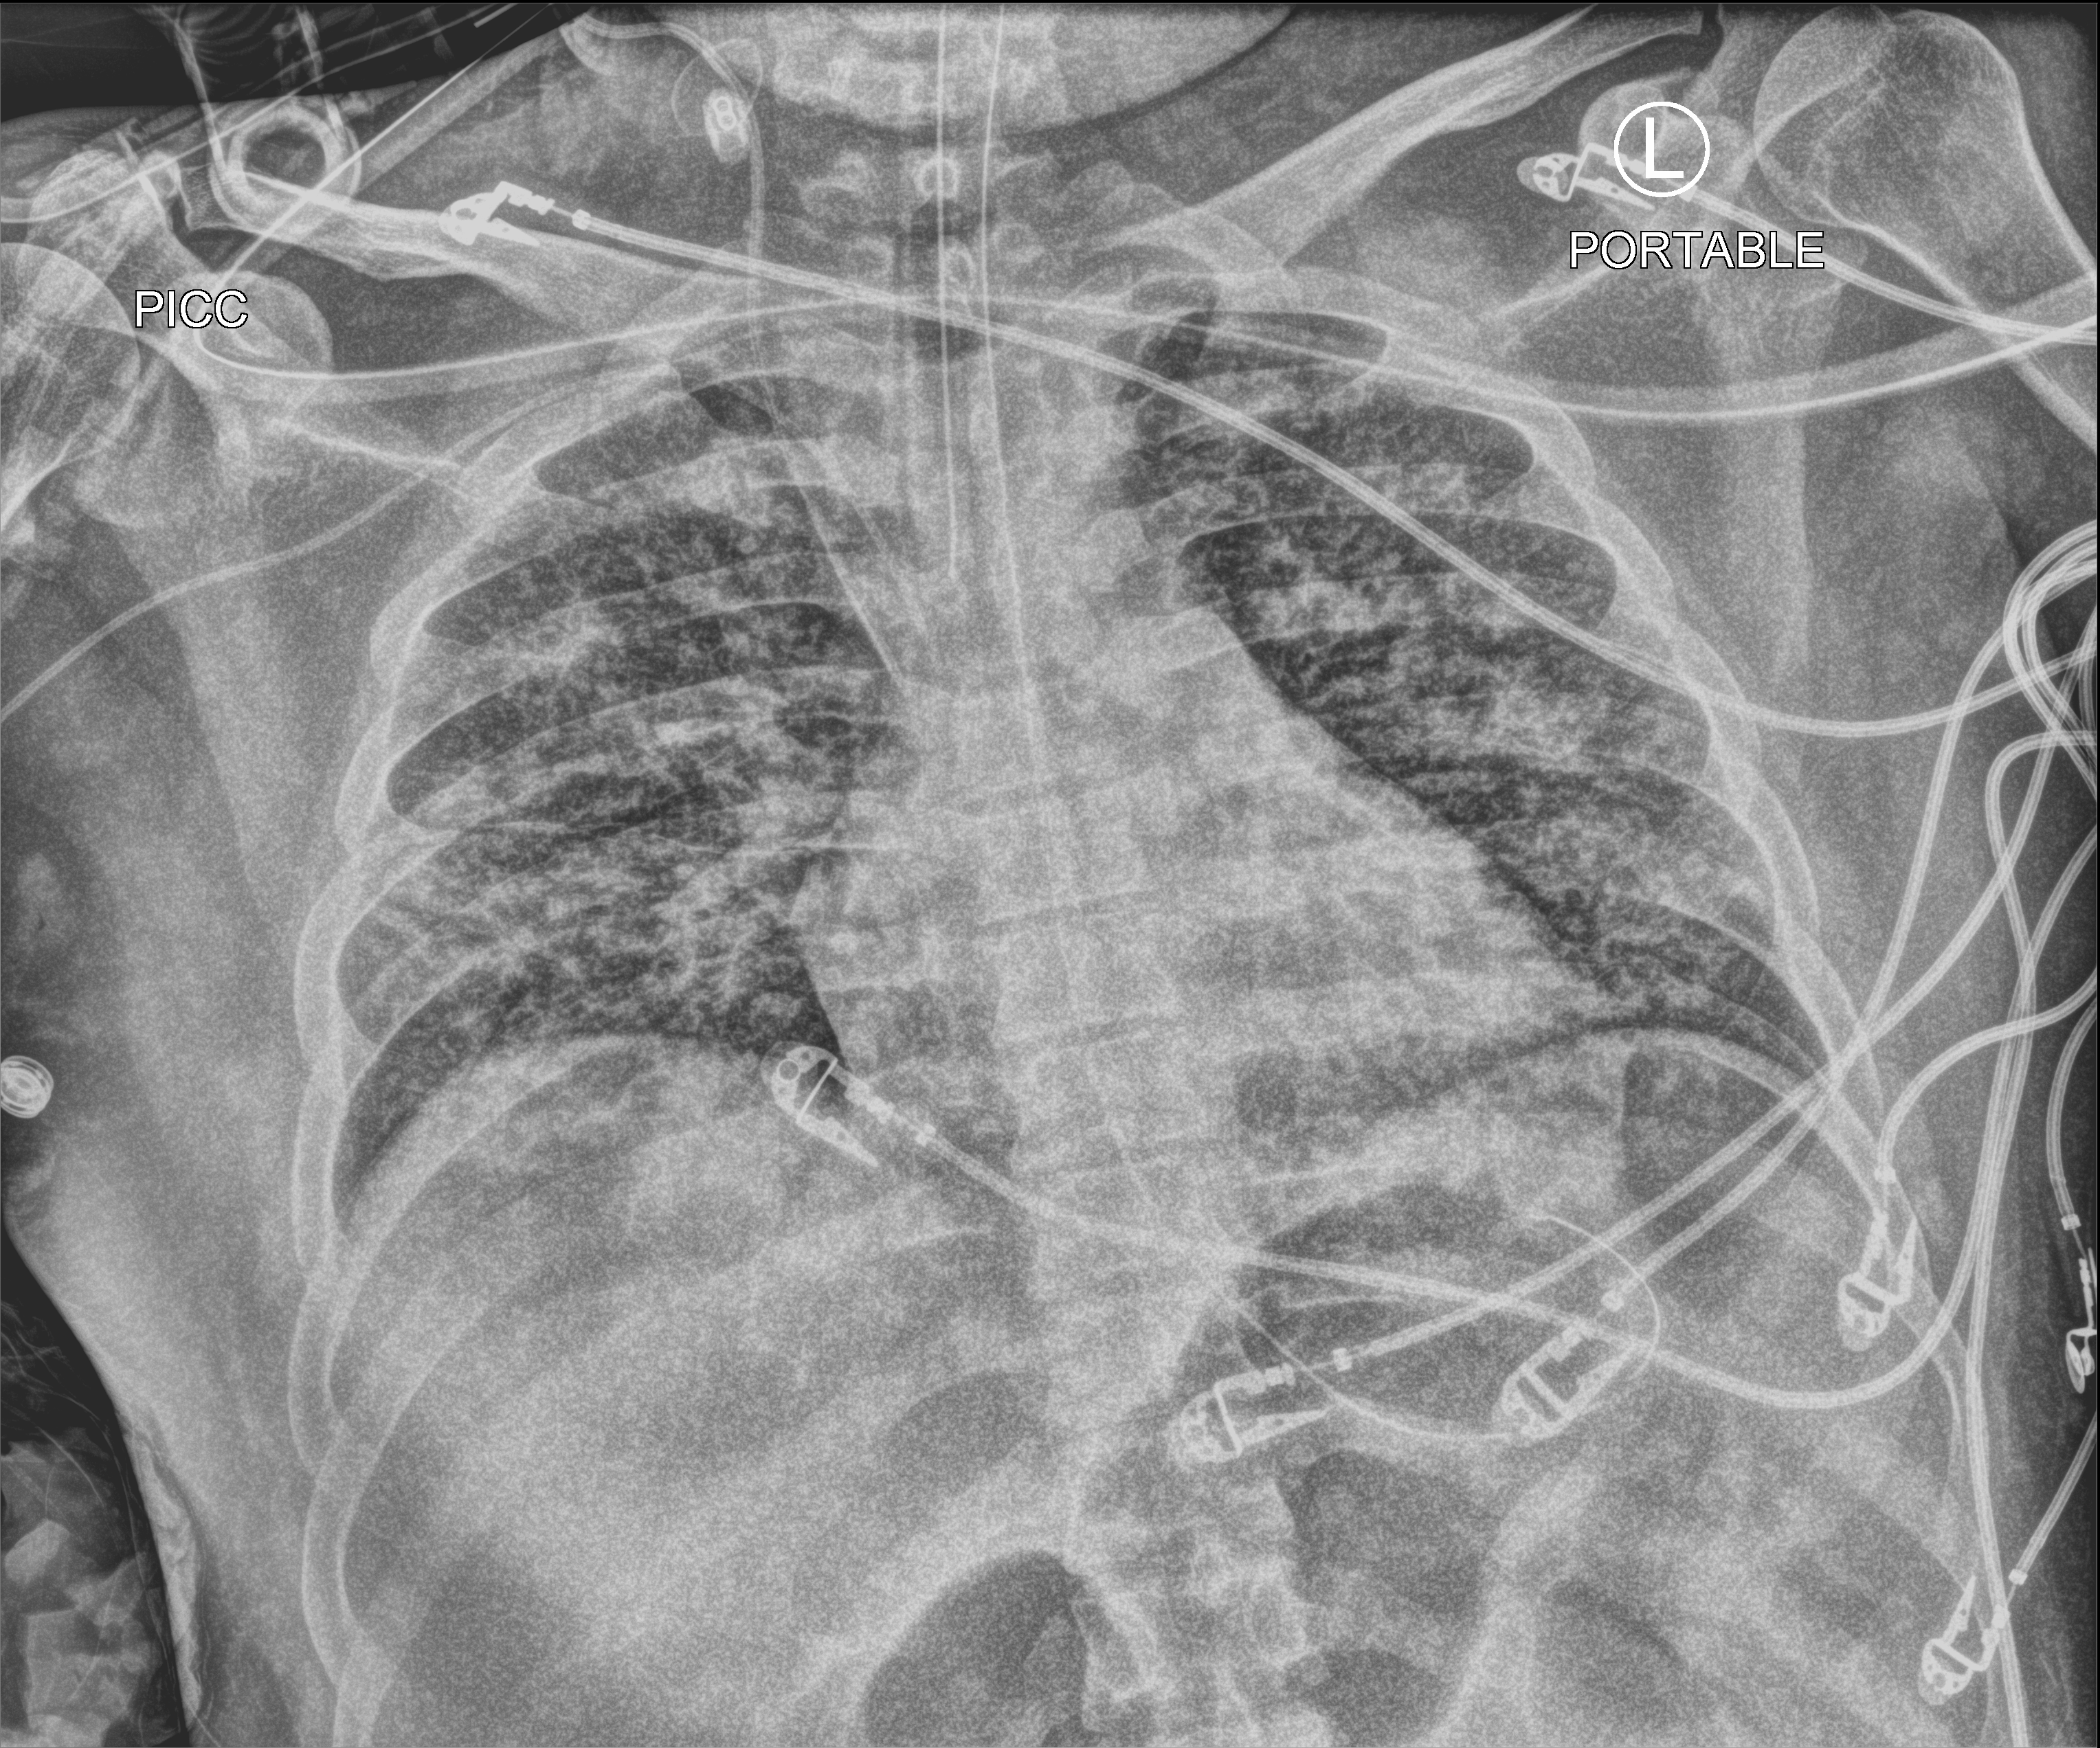
Portable chest radiograph; anteroposterior (AP) projection. Male patient hospitalised with COVID-19, age 18–59 years.
Admission-level facts for this patient (not findings on this image; timing relative to this image not recorded): admitted to intensive care during this hospital stay: yes.